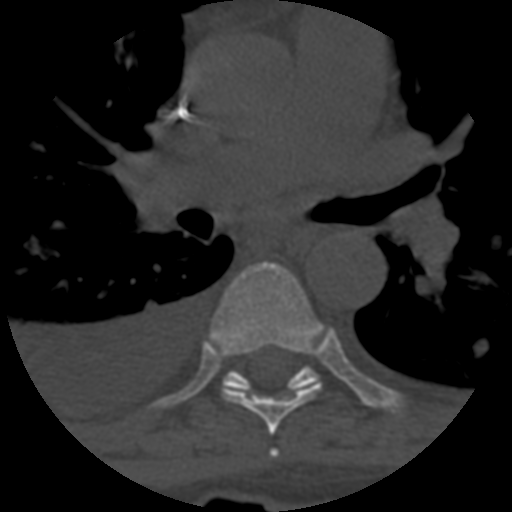
CT including the spine, one axial slice; slice 429 of 708 in the series (ordered by position); one of 3 acquisitions stored at this slice position; bone window (W 1800 / L 400 HU); 1.25 mm slice thickness; 512 × 512 image matrix. Patient age 55 years. From the clinical record (not read from this slice): primary cancer: colon.
Annotated regions visible in this slice (semi-automatic segmentation, software-assisted and operator-edited):
- T5 vertebra: bounding box <269,449,279,458> (left, top, right, bottom; pixels)
- T6 vertebra: <211,261,321,435>
- T7 vertebra: <222,366,318,391>